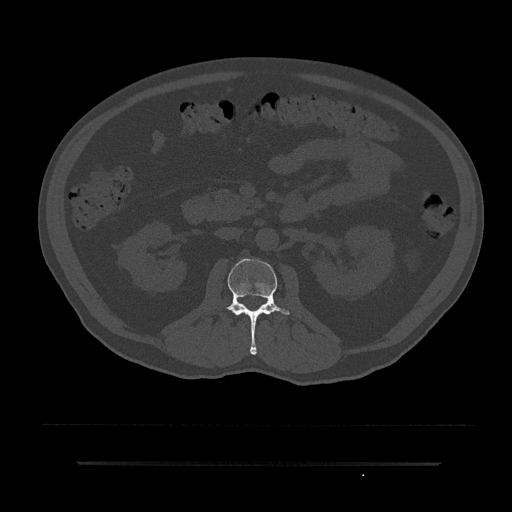
CT including the spine, one axial slice; position 74 of 797 along the scan axis; reconstruction kernel Br40s/3; 120 kVp; bone window (W 1800 / L 400 HU); 0.5 mm slice thickness; 512 × 512 image matrix. Patient: male, 59 years. Case-level facts recorded for this patient, not image findings: primary cancer: bile ducts; vertebrae with lytic lesions (as recorded): T10.
Outlined on this slice (semi-automatic segmentation, software-assisted and operator-edited):
- L2 vertebra: box from (x=225, y=258) to (x=291, y=355) px